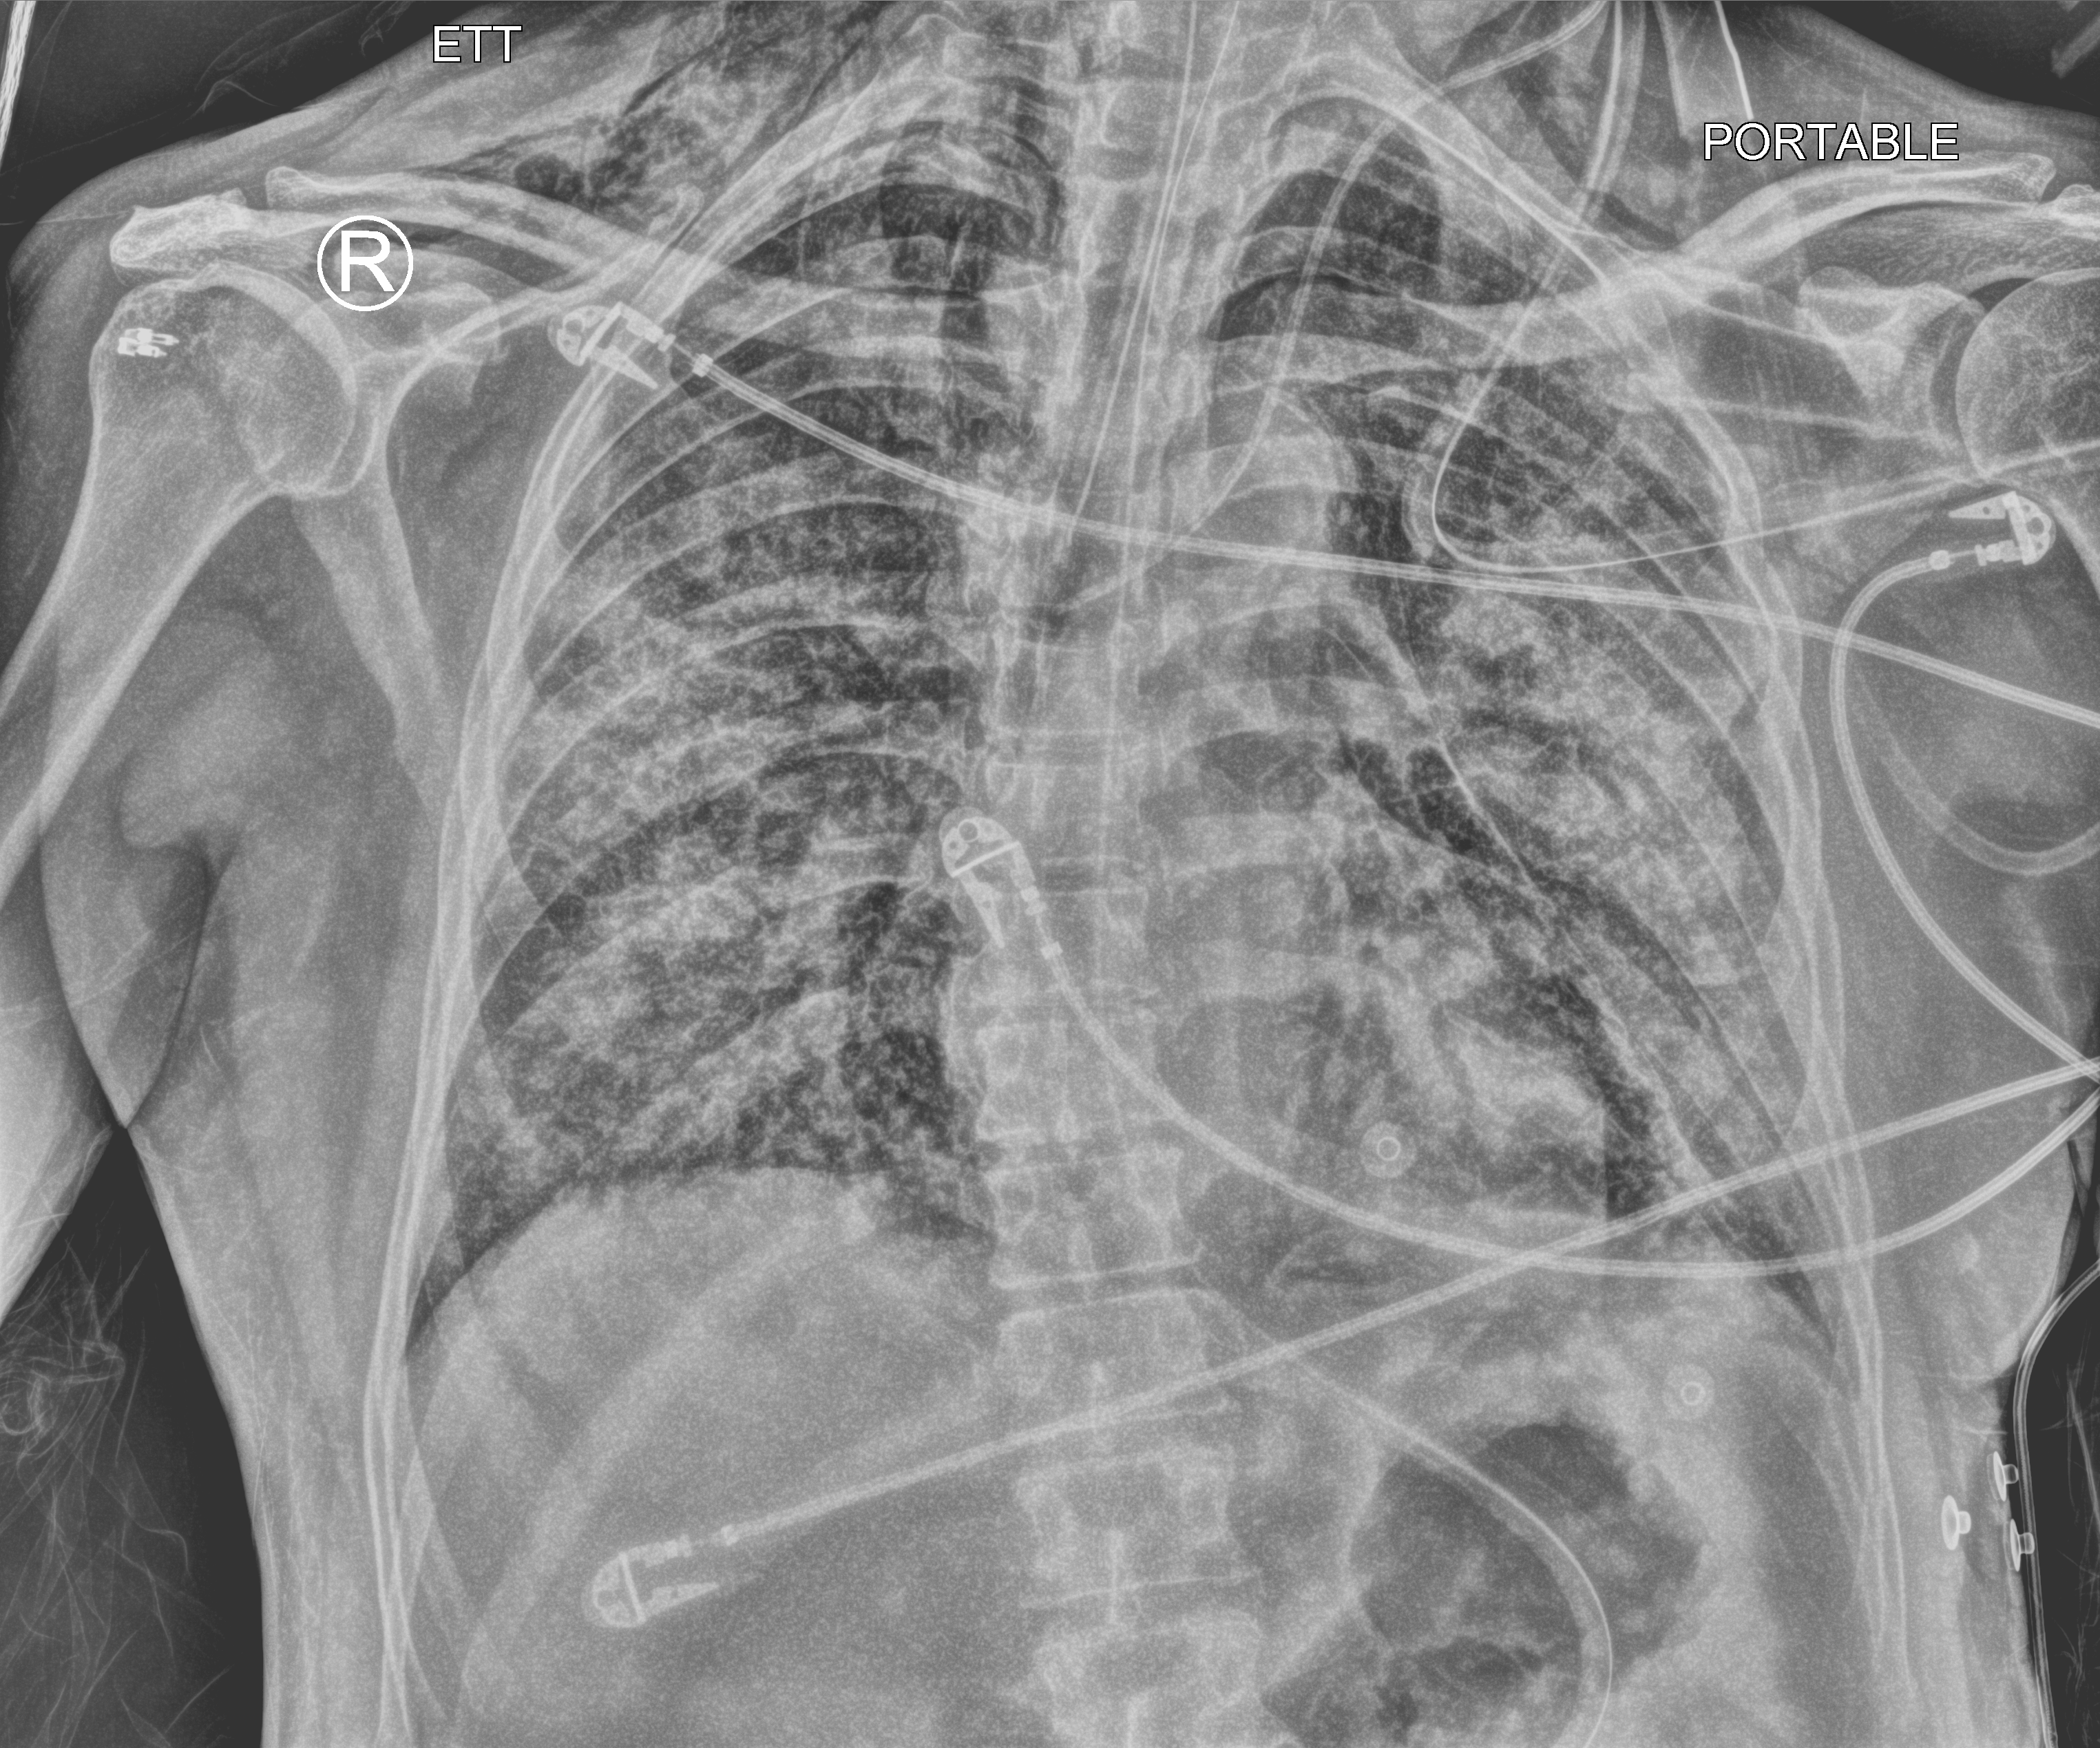
Chest X-ray (portable). Patient hospitalised with COVID-19; male, aged 60–74 years.
Hospital-stay facts (about this admission, not read from this image; timing relative to this image not recorded): COPD (admission record): no.